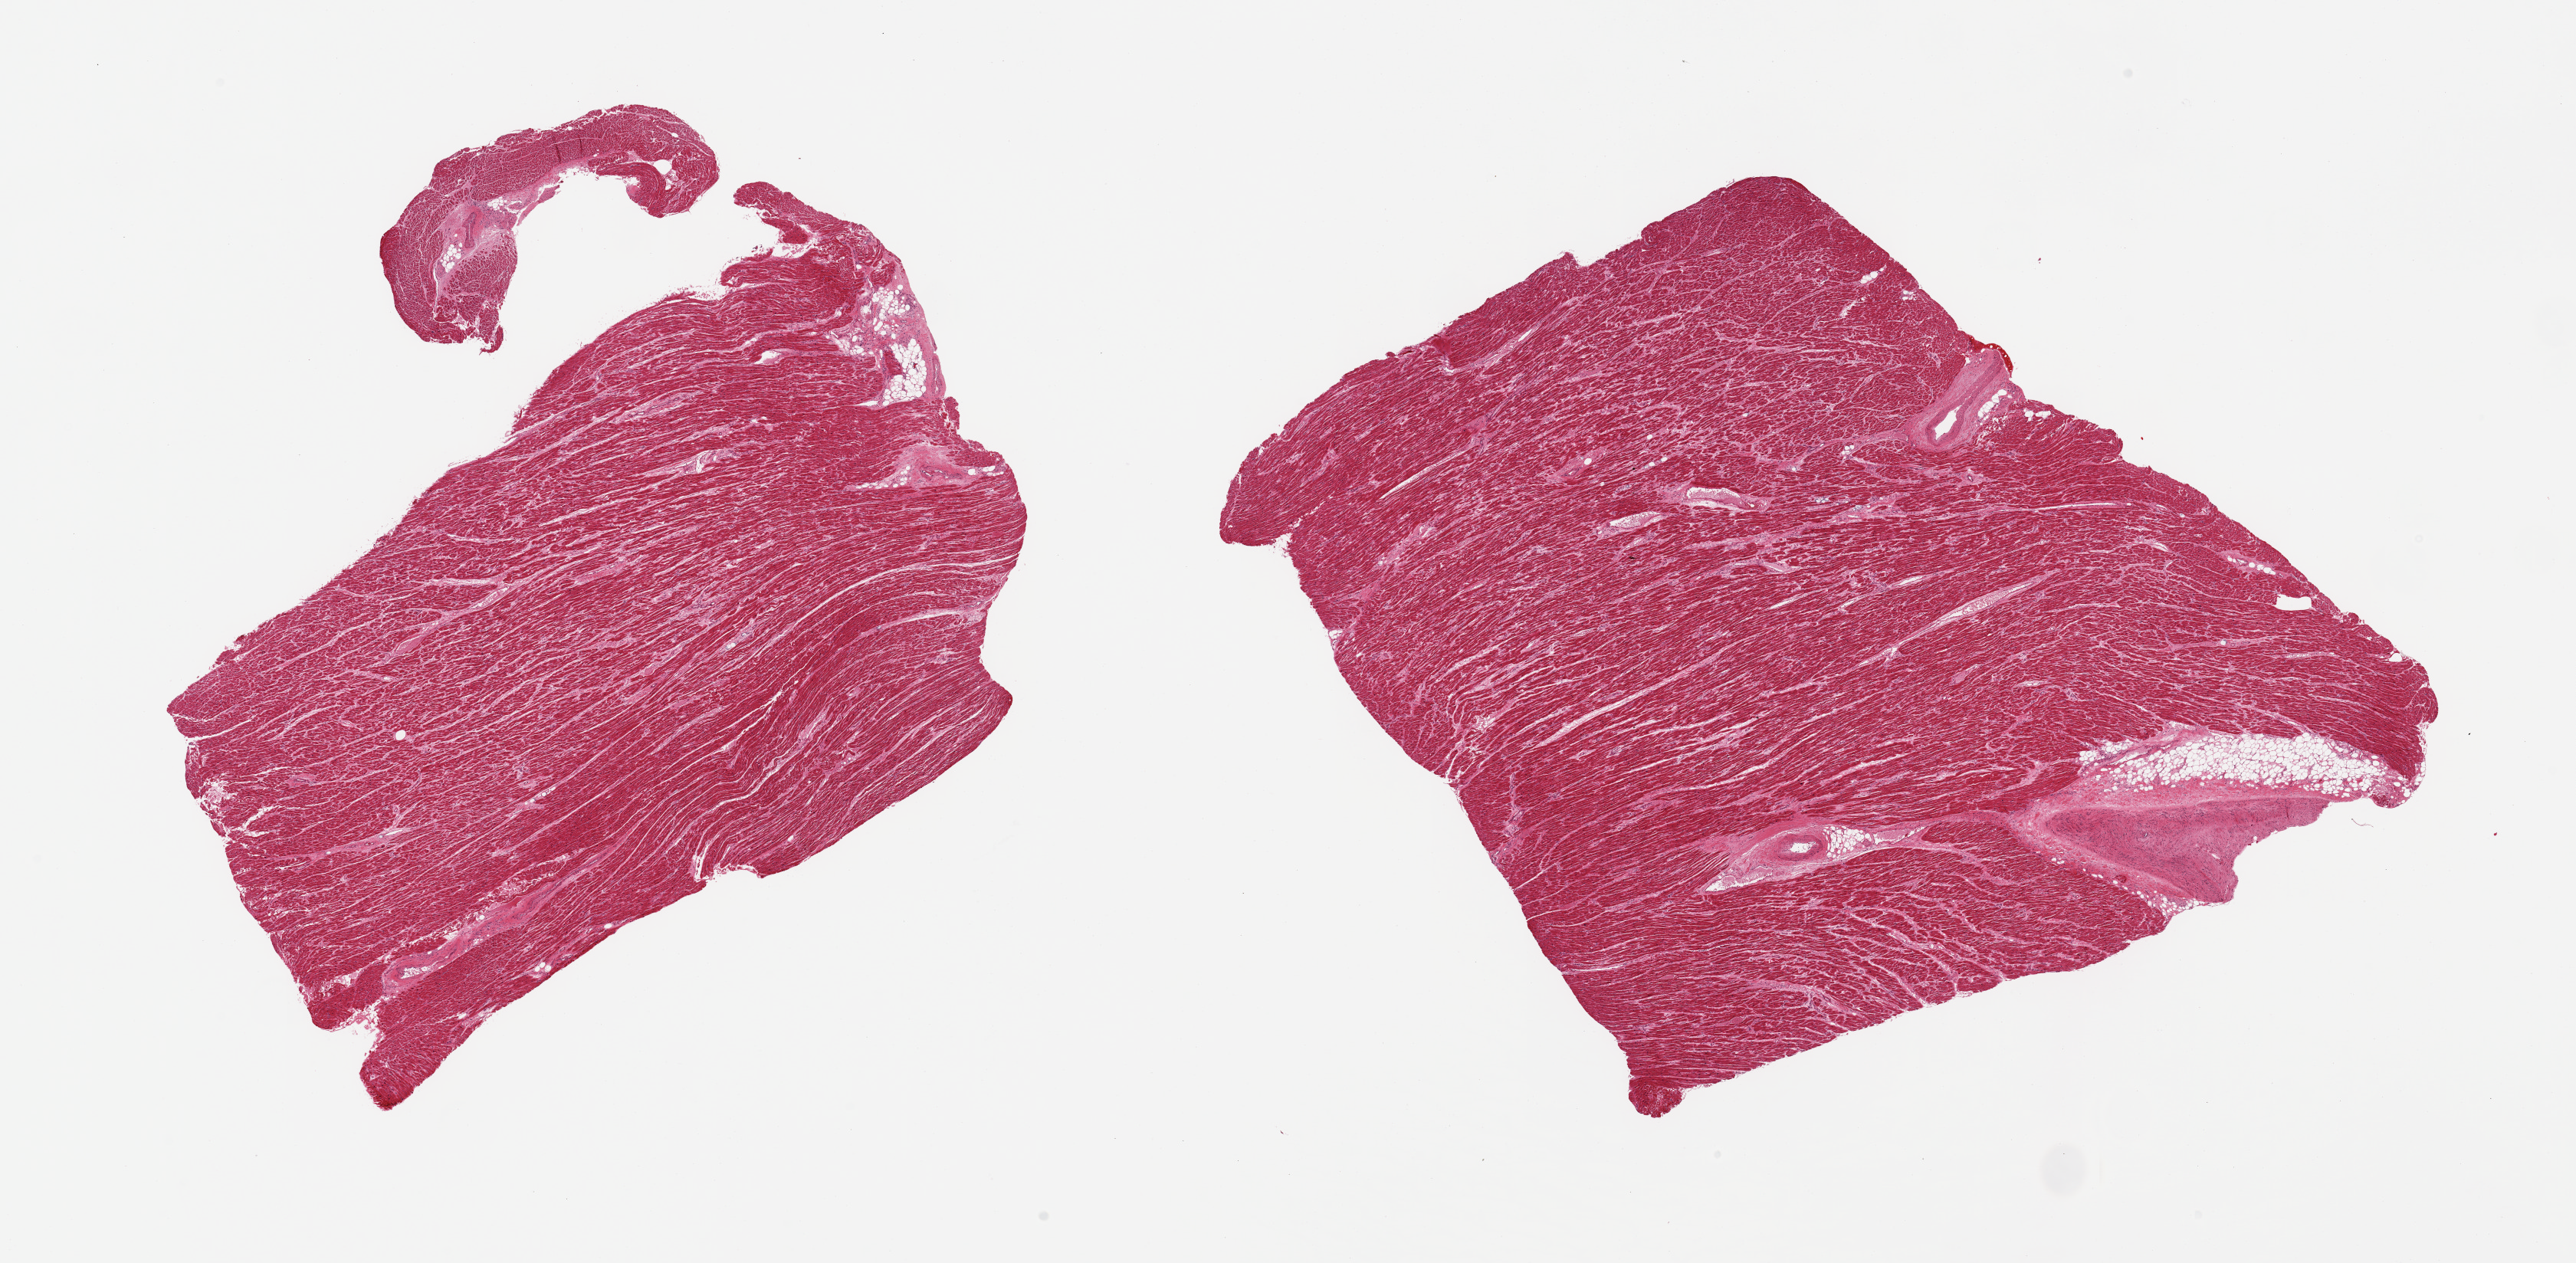
H&E whole-slide image — whole scanned area (about 26.6 x 13.0 mm) shown as a low-resolution overview. PAXgene-fixed paraffin-embedded (PFPE) section. Target tissue: heart. Donor tissue sample. Donor sex: male.
Review note (as recorded): 2 pieces.